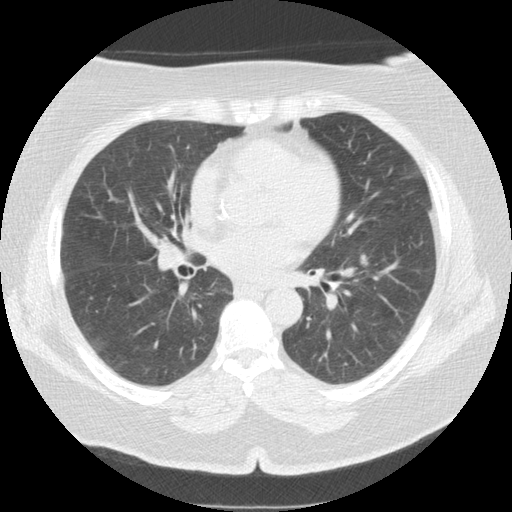
Chest CT (low-dose screening protocol), one axial image; baseline annual screen; lung window (W 1500 / L -600 HU); 2.5 mm slice thickness; standard (soft-tissue) reconstruction kernel (STANDARD); 120 kVp; slice 77 of 161 in the series. Female, age 65 years at enrolment. Current smoker at enrolment.
Expert-annotated lung lesion, bounding box (x1, y1, x2, y2) in pixels: (348, 244, 378, 276). No non-calcified nodule or mass ≥4 mm was recorded by the screening reader at this exam. Participant outcome: lung cancer diagnosed 986 days after this screen — adenocarcinoma, NOS, left lower lobe, moderately differentiated (G2), stage IA (AJCC 6th edition), 12 mm at pathology.